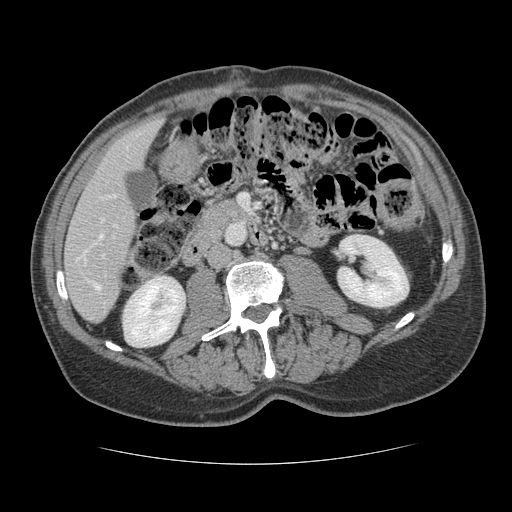
Contrast-enhanced abdominal CT, one axial slice. Position 46 of 134 along the scan axis. Reconstruction kernel STANDARD. Intravenous contrast given. Soft-tissue window (W 400 / L 40 HU). 2.5 mm slice thickness. 512 × 512 image matrix, field of view 377 × 377 mm. Male patient, age 68 years. Case-level facts recorded for this patient, not image findings: diagnosis: colorectal cancer liver metastases, imaged before liver resection; multiple liver metastases: yes; largest metastasis: 2.2 cm.
Annotated regions visible in this slice (expert manual segmentation):
- hepatic veins: bounding box (x1, y1, x2, y2) in pixels: (99, 195, 115, 238)
- liver: (65, 119, 162, 322)
- planned liver remnant (the part of the liver to remain after resection): (65, 119, 162, 322)
- portal vein (with intrahepatic branches): (93, 255, 104, 290)